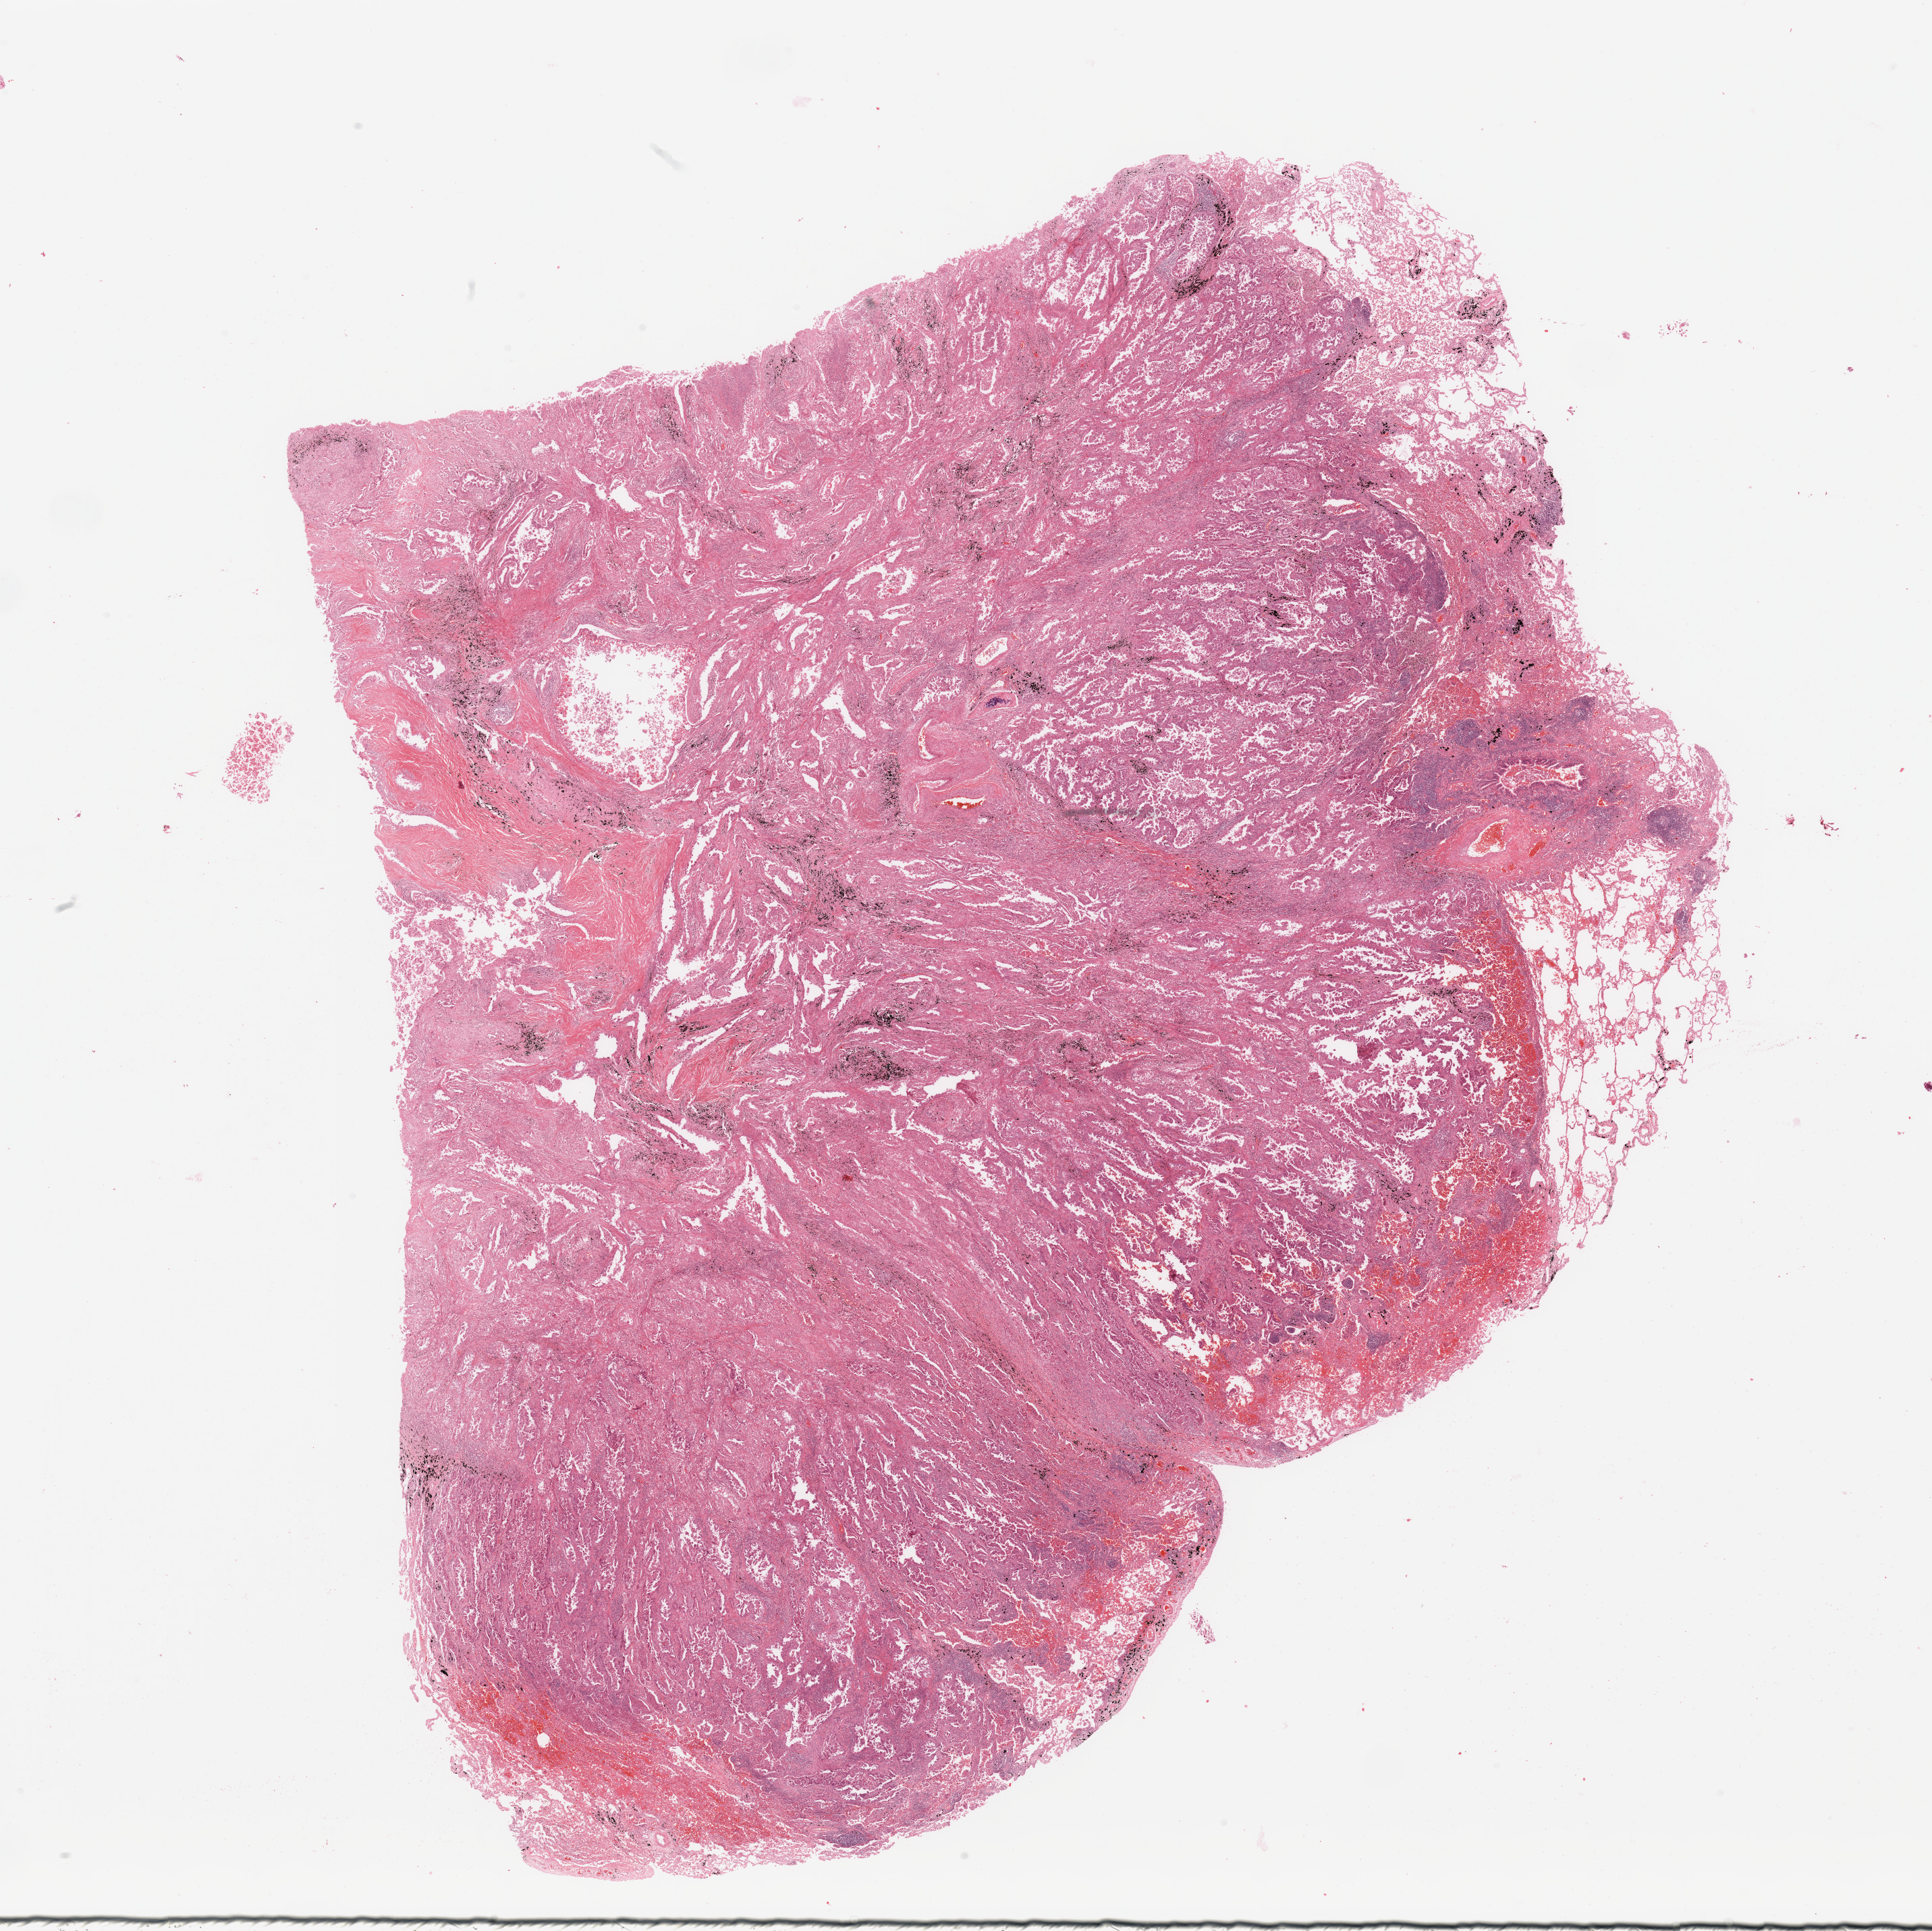
Digitized Hematoxylin and eosin (H&E) stained tissue section (whole slide), shown as a low-resolution overview of the whole scanned area (about 22.6 x 22.6 mm, acquisition: 20x scan). Lung, tumour tissue. Male, 65 y/o. Histologic grade: G3 (poorly differentiated).
Histologic diagnosis: Adenocarcinoma, NOS. AJCC pathologic stage: IB.